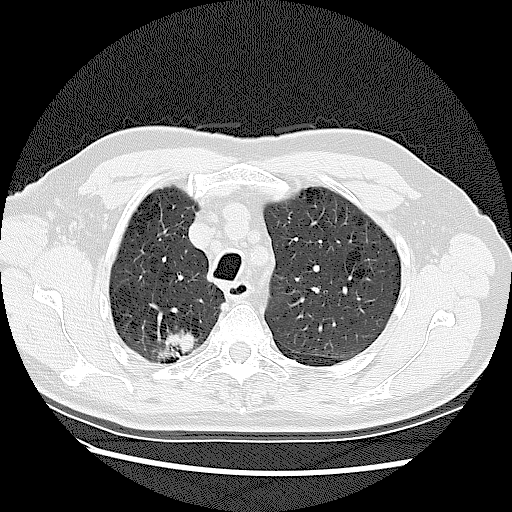
Low-dose screening chest CT, one axial slice; slice 99 of 128 in the series (ordered by position); lung window (W 1500 / L -600 HU); 2.5 mm slice thickness; 512 × 512 image matrix.
Outlined on this slice (expert manual segmentation):
- lesion 2 (tumor, upper lobe of right lung): box from (x=166, y=334) to (x=194, y=353) px